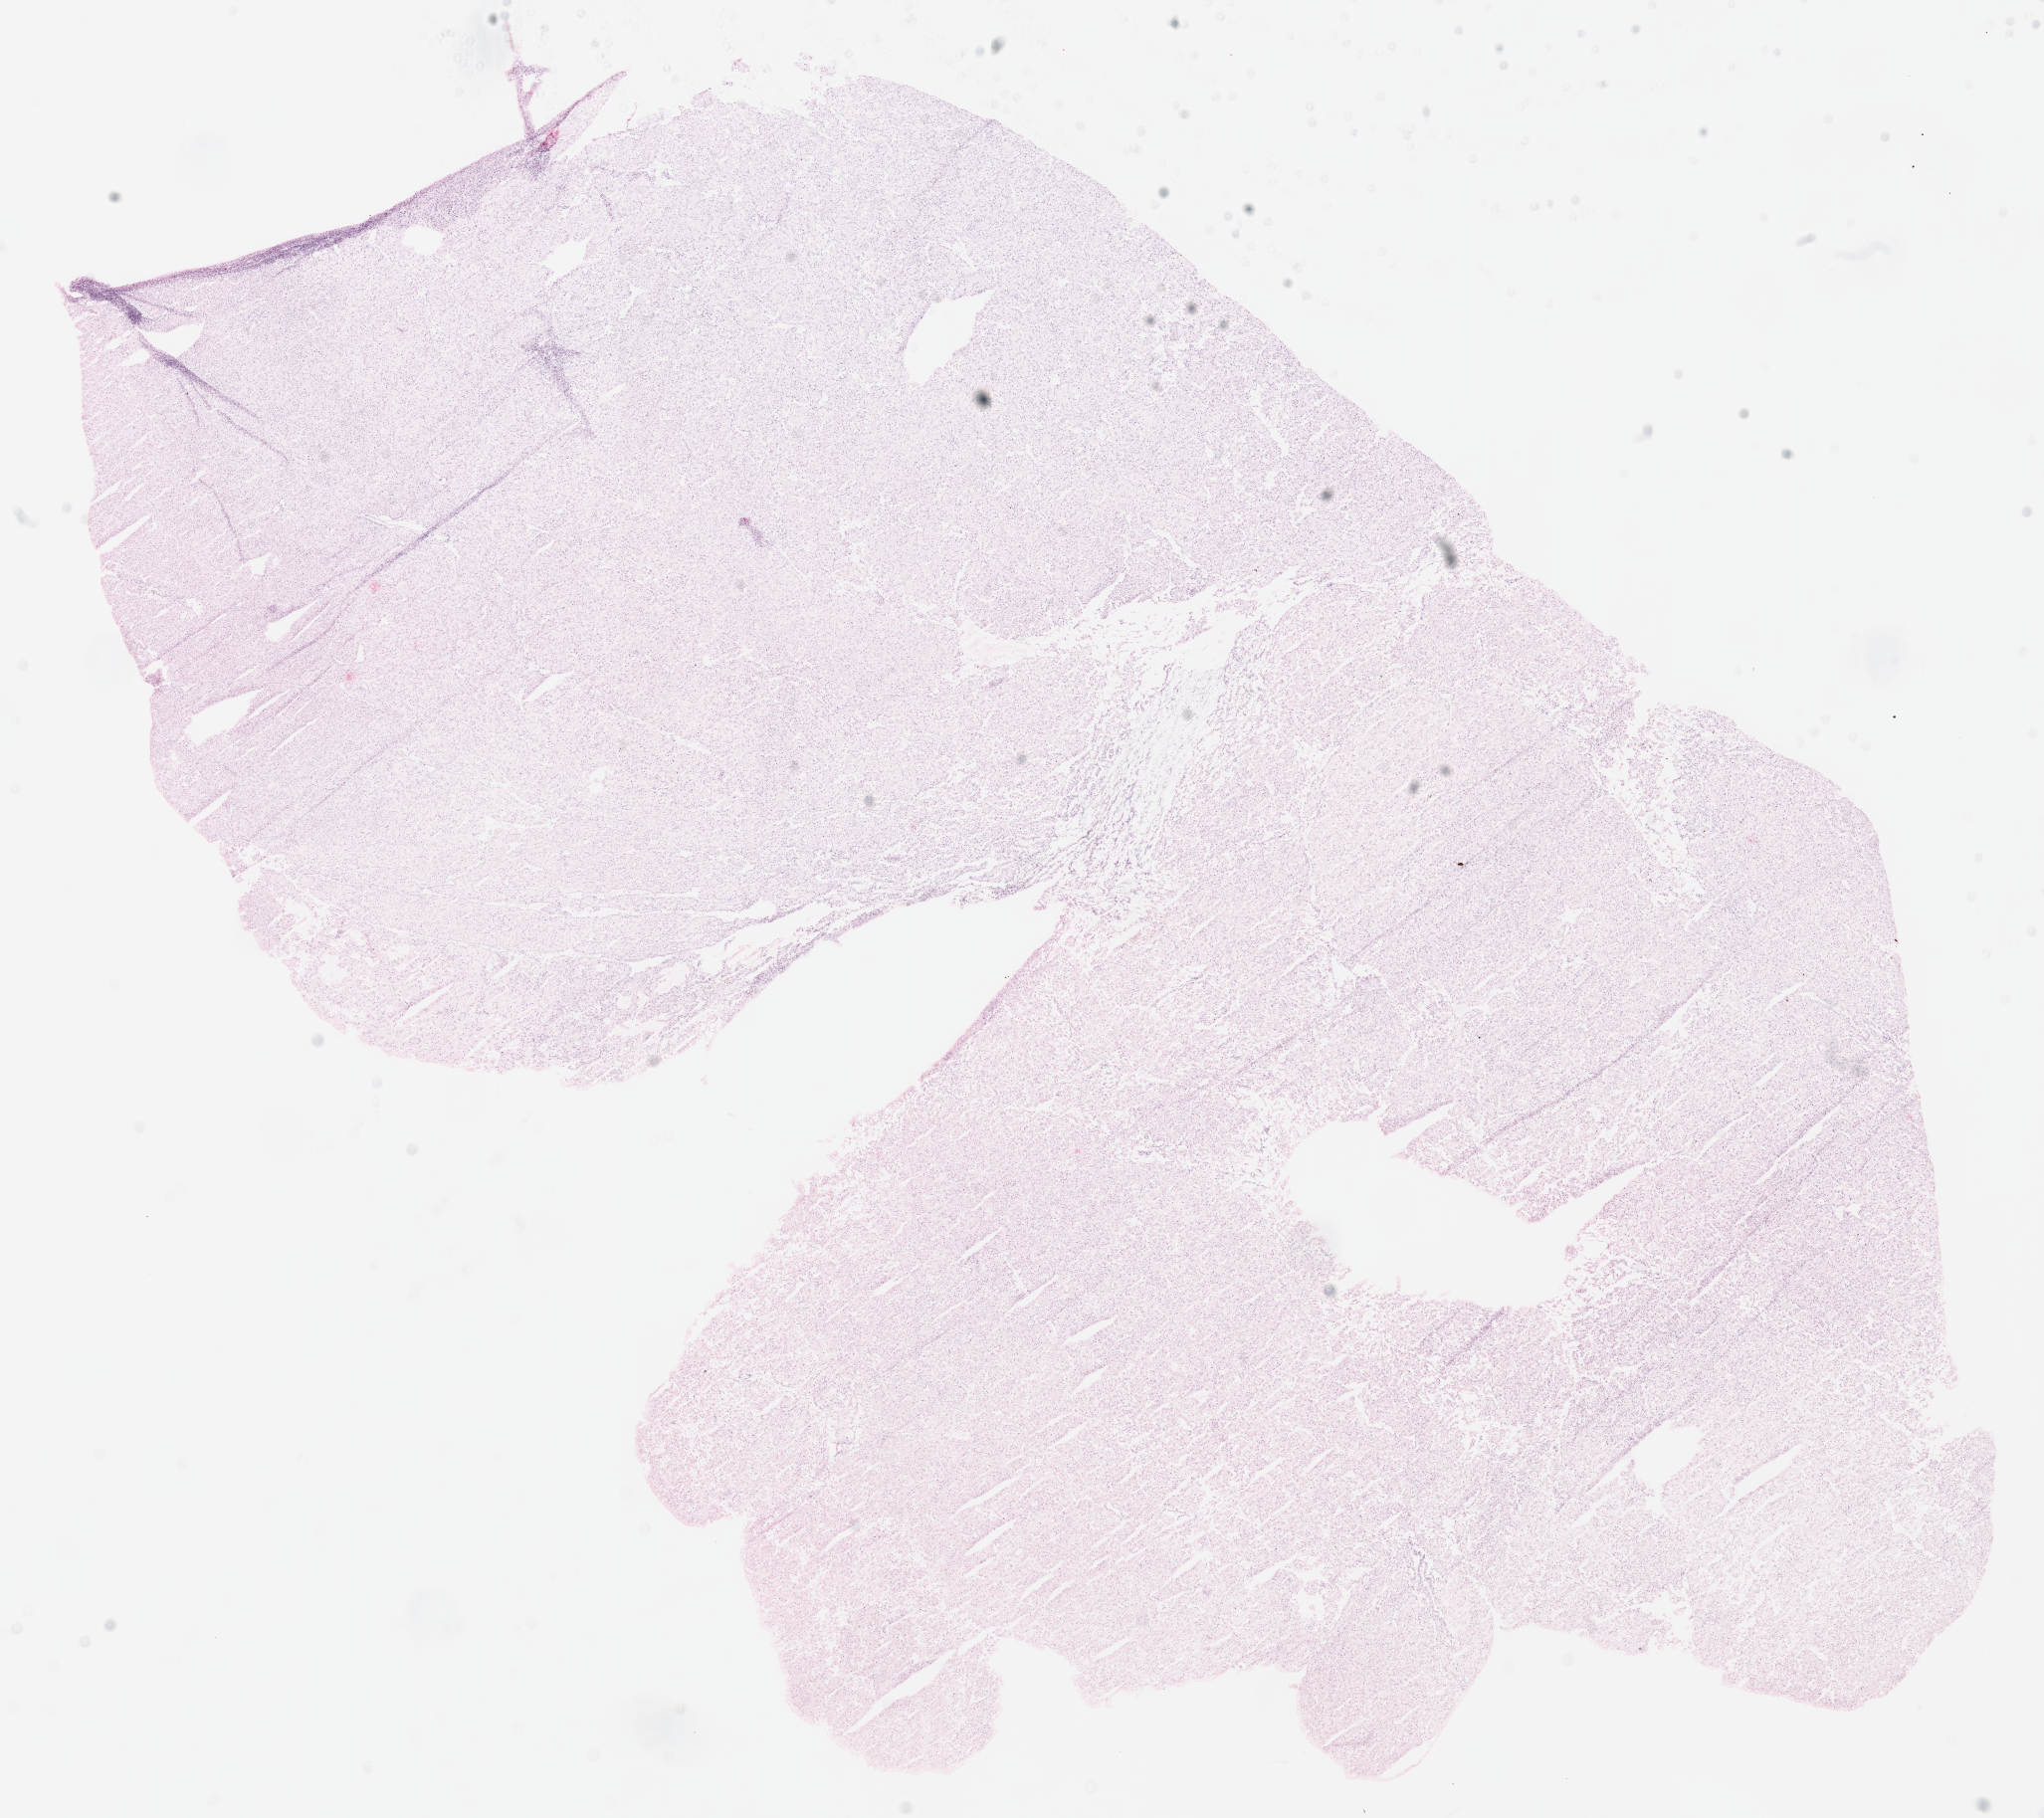
Whole-slide histology image, H&E, low-resolution overview of the scanned area, about 16.2 x 14.4 mm (slide scanned at 40x); frozen section from the top of the tissue portion; sample: primary tumour, kidney. Male, age 50 years at initial diagnosis.
Histologic diagnosis: Renal cell carcinoma, chromophobe type.